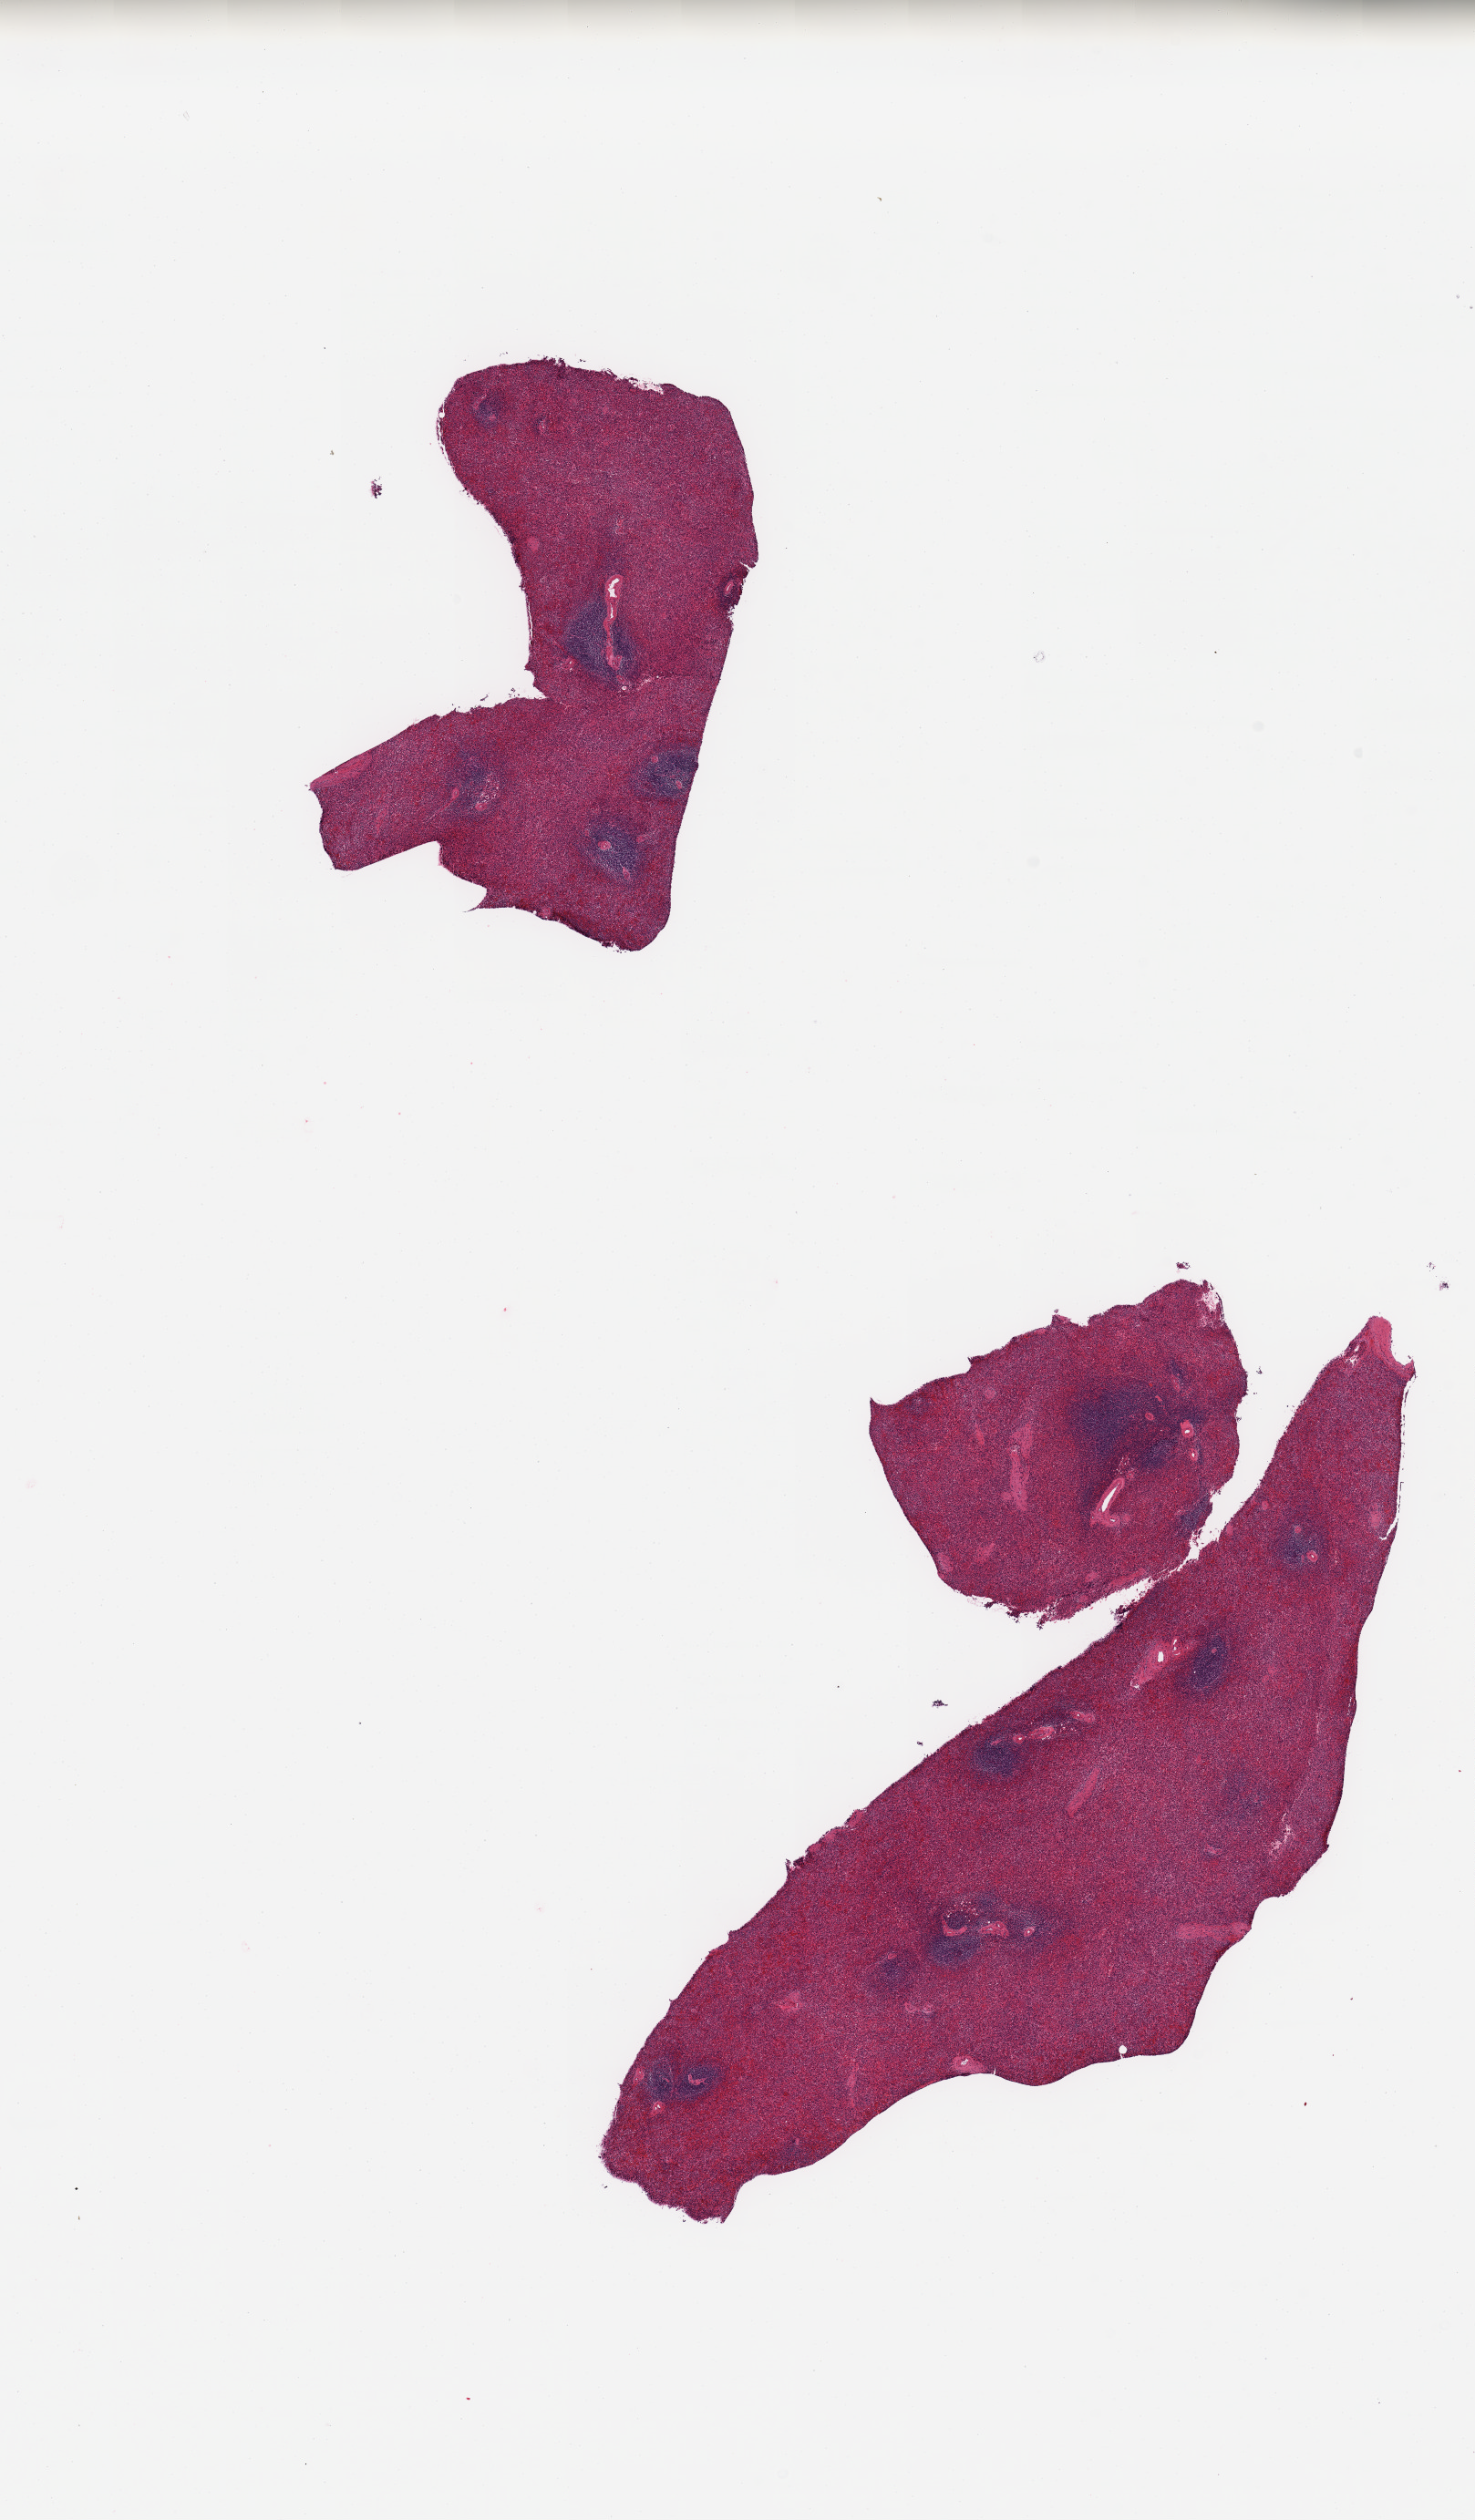
Whole-slide image, H&E stain, whole scanned area (about 12.8 x 21.9 mm, acquisition: 20x scan) shown as a low-resolution overview, PAXgene-fixed paraffin-embedded (PFPE) section, section of spleen (target tissue), tissue donor sample. Donor sex: female.
Pathologist's review note for this sample: 2 pieces; congestion.